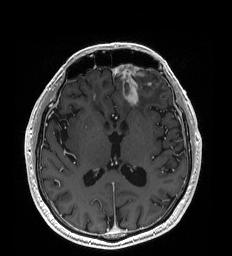
Brain MRI from a brain-tumour surgery series, one axial slice; position 100 of 192 along the scan axis; T1-weighted post-contrast; 232 × 256 image matrix, field of view 227 × 250 mm. From the clinical record (not read from this slice): histopathology: Glioblastoma; WHO grade: 4; IDH mutation: no.
Structures marked on this image (manually delineated by an expert):
- tumour: bounding box [x1, y1, x2, y2] px = [124, 86, 139, 105]